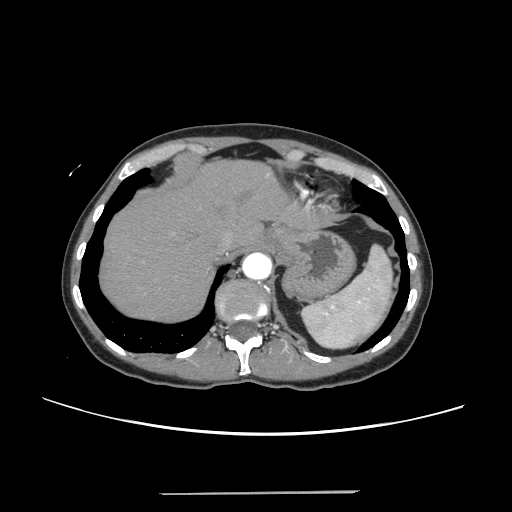
Contrast-enhanced abdominal CT, one axial slice. Position 203 of 240 along the scan axis. Intravenous contrast given. Soft-tissue window (W 400 / L 40 HU). 1.25 mm slice thickness. 512 × 512 image matrix, field of view 371 × 371 mm. Female patient, age 60 years. From the clinical record (not read from this slice): diagnosis: colorectal cancer liver metastases, imaged before liver resection; multiple liver metastases: no; largest metastasis: 1.5 cm.
Structures marked on this image (expert manual segmentation):
- hepatic veins: bounding box <220,220,250,251> (left, top, right, bottom; pixels)
- liver: <100,161,315,320>
- planned liver remnant (the part of the liver to remain after resection): <100,161,309,320>